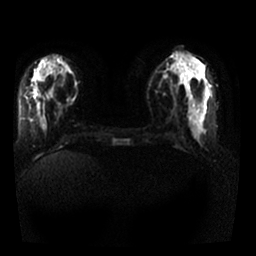
Breast MRI, one axial slice; position 10 of 25 along the scan axis; diffusion-weighted series; image 2 of 4 stored at this slice position (different b-values; order by instance number); 1.5 T; 256 × 256 image matrix, field of view 330 × 330 mm. Female patient.
Outlined on this slice (expert manual segmentation):
- tumour on diffusion-weighted imaging: bounding box [x1, y1, x2, y2] px = [33, 76, 38, 80]